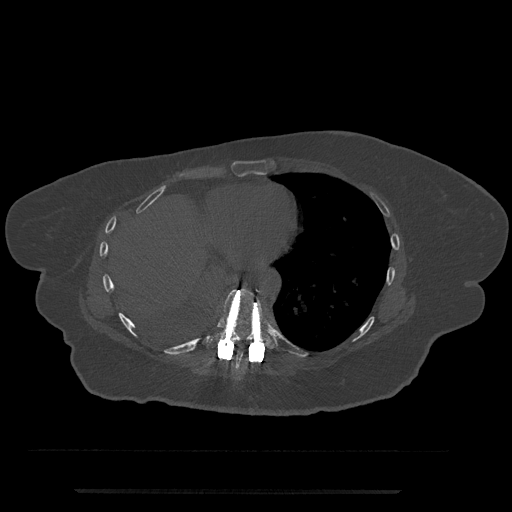
CT including the spine, one axial slice; position 353 of 797 along the scan axis; reconstruction kernel Br40s/3; bone window (W 1800 / L 400 HU); 512 × 512 image matrix, field of view 440 × 440 mm. Female patient, age 51 years. Case-level facts recorded for this patient, not image findings: primary cancer: neuro.
Outlined on this slice (semi-automatic segmentation, software-assisted and operator-edited):
- T8 vertebra: bounding box [x1, y1, x2, y2] px = [232, 346, 250, 373]
- T9 vertebra: [204, 287, 276, 362]